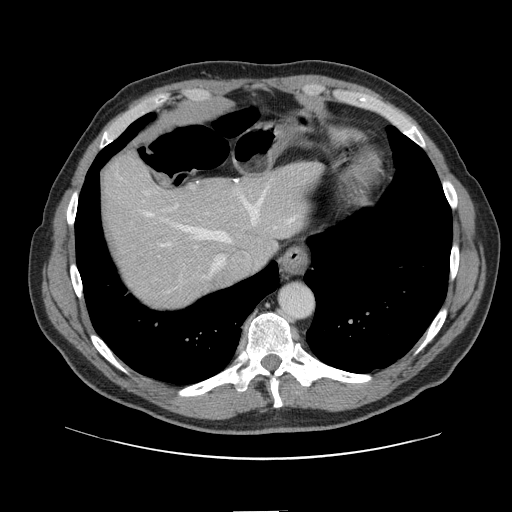
Contrast-enhanced abdominal CT, one axial slice. Position 122 of 161 along the scan axis. Intravenous contrast given. Soft-tissue window (W 400 / L 40 HU). 2.5 mm slice thickness. 512 × 512 image matrix, field of view 412 × 412 mm. Male patient, age 66 years. Case-level facts recorded for this patient, not image findings: diagnosis: colorectal cancer liver metastases, imaged before liver resection; multiple liver metastases: no; largest metastasis: 3.5 cm; disease in both lobes: no.
Outlined on this slice (expert manual segmentation):
- hepatic veins: box from (x=117, y=175) to (x=297, y=292) px
- liver: (x=102, y=155)–(x=314, y=307)
- planned liver remnant (the part of the liver to remain after resection): (x=102, y=155)–(x=315, y=296)
- liver metastasis: (x=210, y=272)–(x=226, y=290)